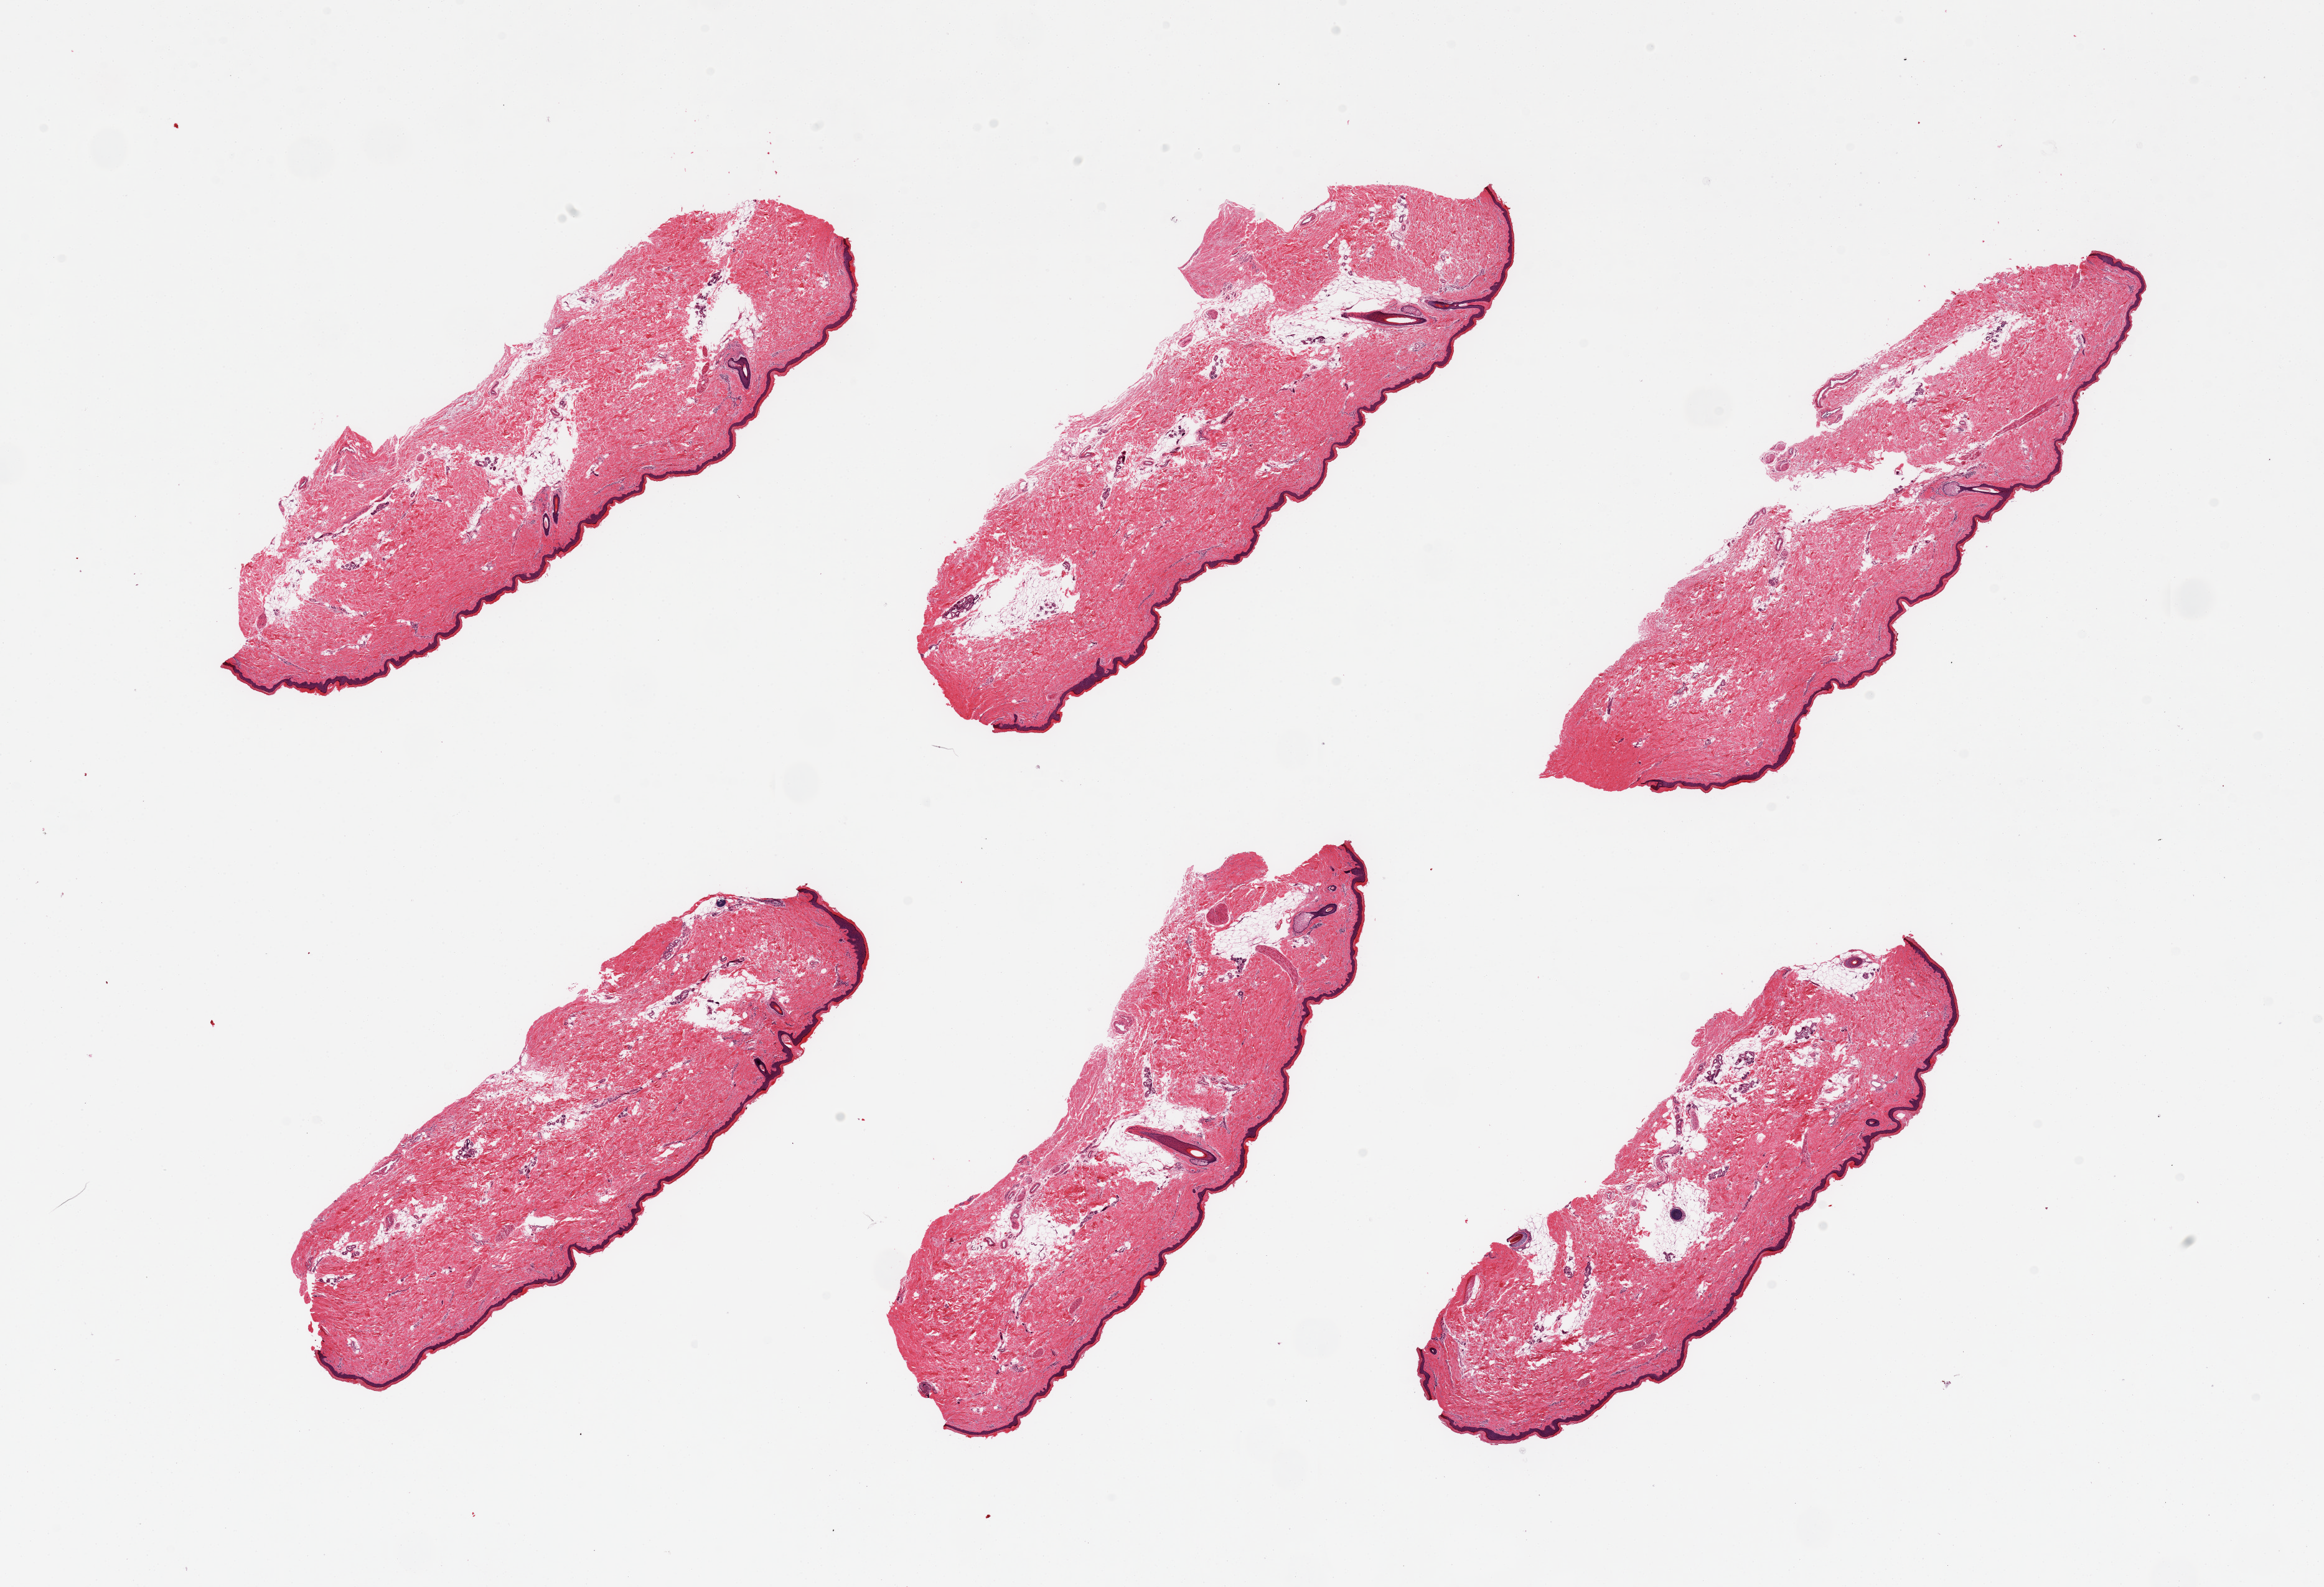
Hematoxylin and eosin (H&E) whole-slide image, brightfield — shown as a low-resolution overview of the whole scanned area (about 29.5 x 20.2 mm), PAXgene-fixed, paraffin-embedded tissue, target tissue: skin of lower leg, donor tissue sample. Donor: female.
- reviewer comment on this tissue sample: 6 pieces; well trimmed; up to 20% intradermal fat